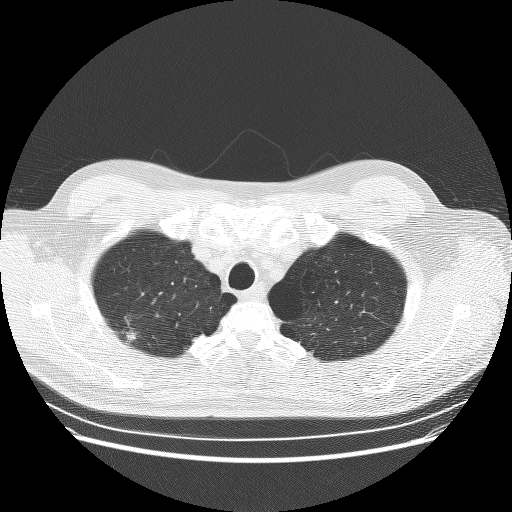
Low-dose screening chest CT, one axial slice. Lung window (W 1500 / L -600 HU). 512 × 512 image matrix.
Annotated regions visible in this slice (manually delineated by an expert):
- lesion 1 (tumor, upper lobe of right lung): bounding box [x1, y1, x2, y2] px = [127, 332, 136, 341]